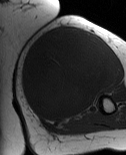
MRI of an extremity soft-tissue mass, one axial slice. MR volume resampled by the dataset authors to the PET/CT grid (not the native acquisition matrix). 3.27 mm slice thickness. 126 × 155 image matrix, field of view 123 × 151 mm. Female patient. From the clinical record (not read from this slice): histological type: pleiomorphic leiomyosarcoma; grade: high; site of the primary tumour: left biceps.
Structures marked on this image (expert contour drawn on MRI and transferred to this co-registered scan by the dataset authors):
- gross tumour volume including surrounding oedema: bounding box [x1, y1, x2, y2] px = [20, 26, 112, 121]
- gross tumour volume (mass): [20, 28, 110, 121]